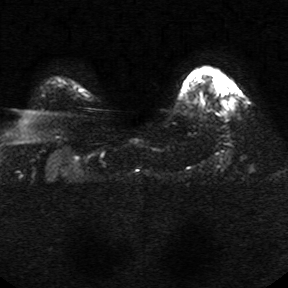
Breast MRI, one axial slice. Position 22 of 34 along the scan axis. Diffusion-weighted series; image 2 of 4 stored at this slice position (different b-values; order by instance number). 1.5 T. 5 mm slice thickness. 288 × 288 image matrix, field of view 340 × 340 mm. Female patient.
Annotated regions visible in this slice (manually delineated by an expert):
- tumour on diffusion-weighted imaging: bounding box <221,99,234,109> (left, top, right, bottom; pixels)